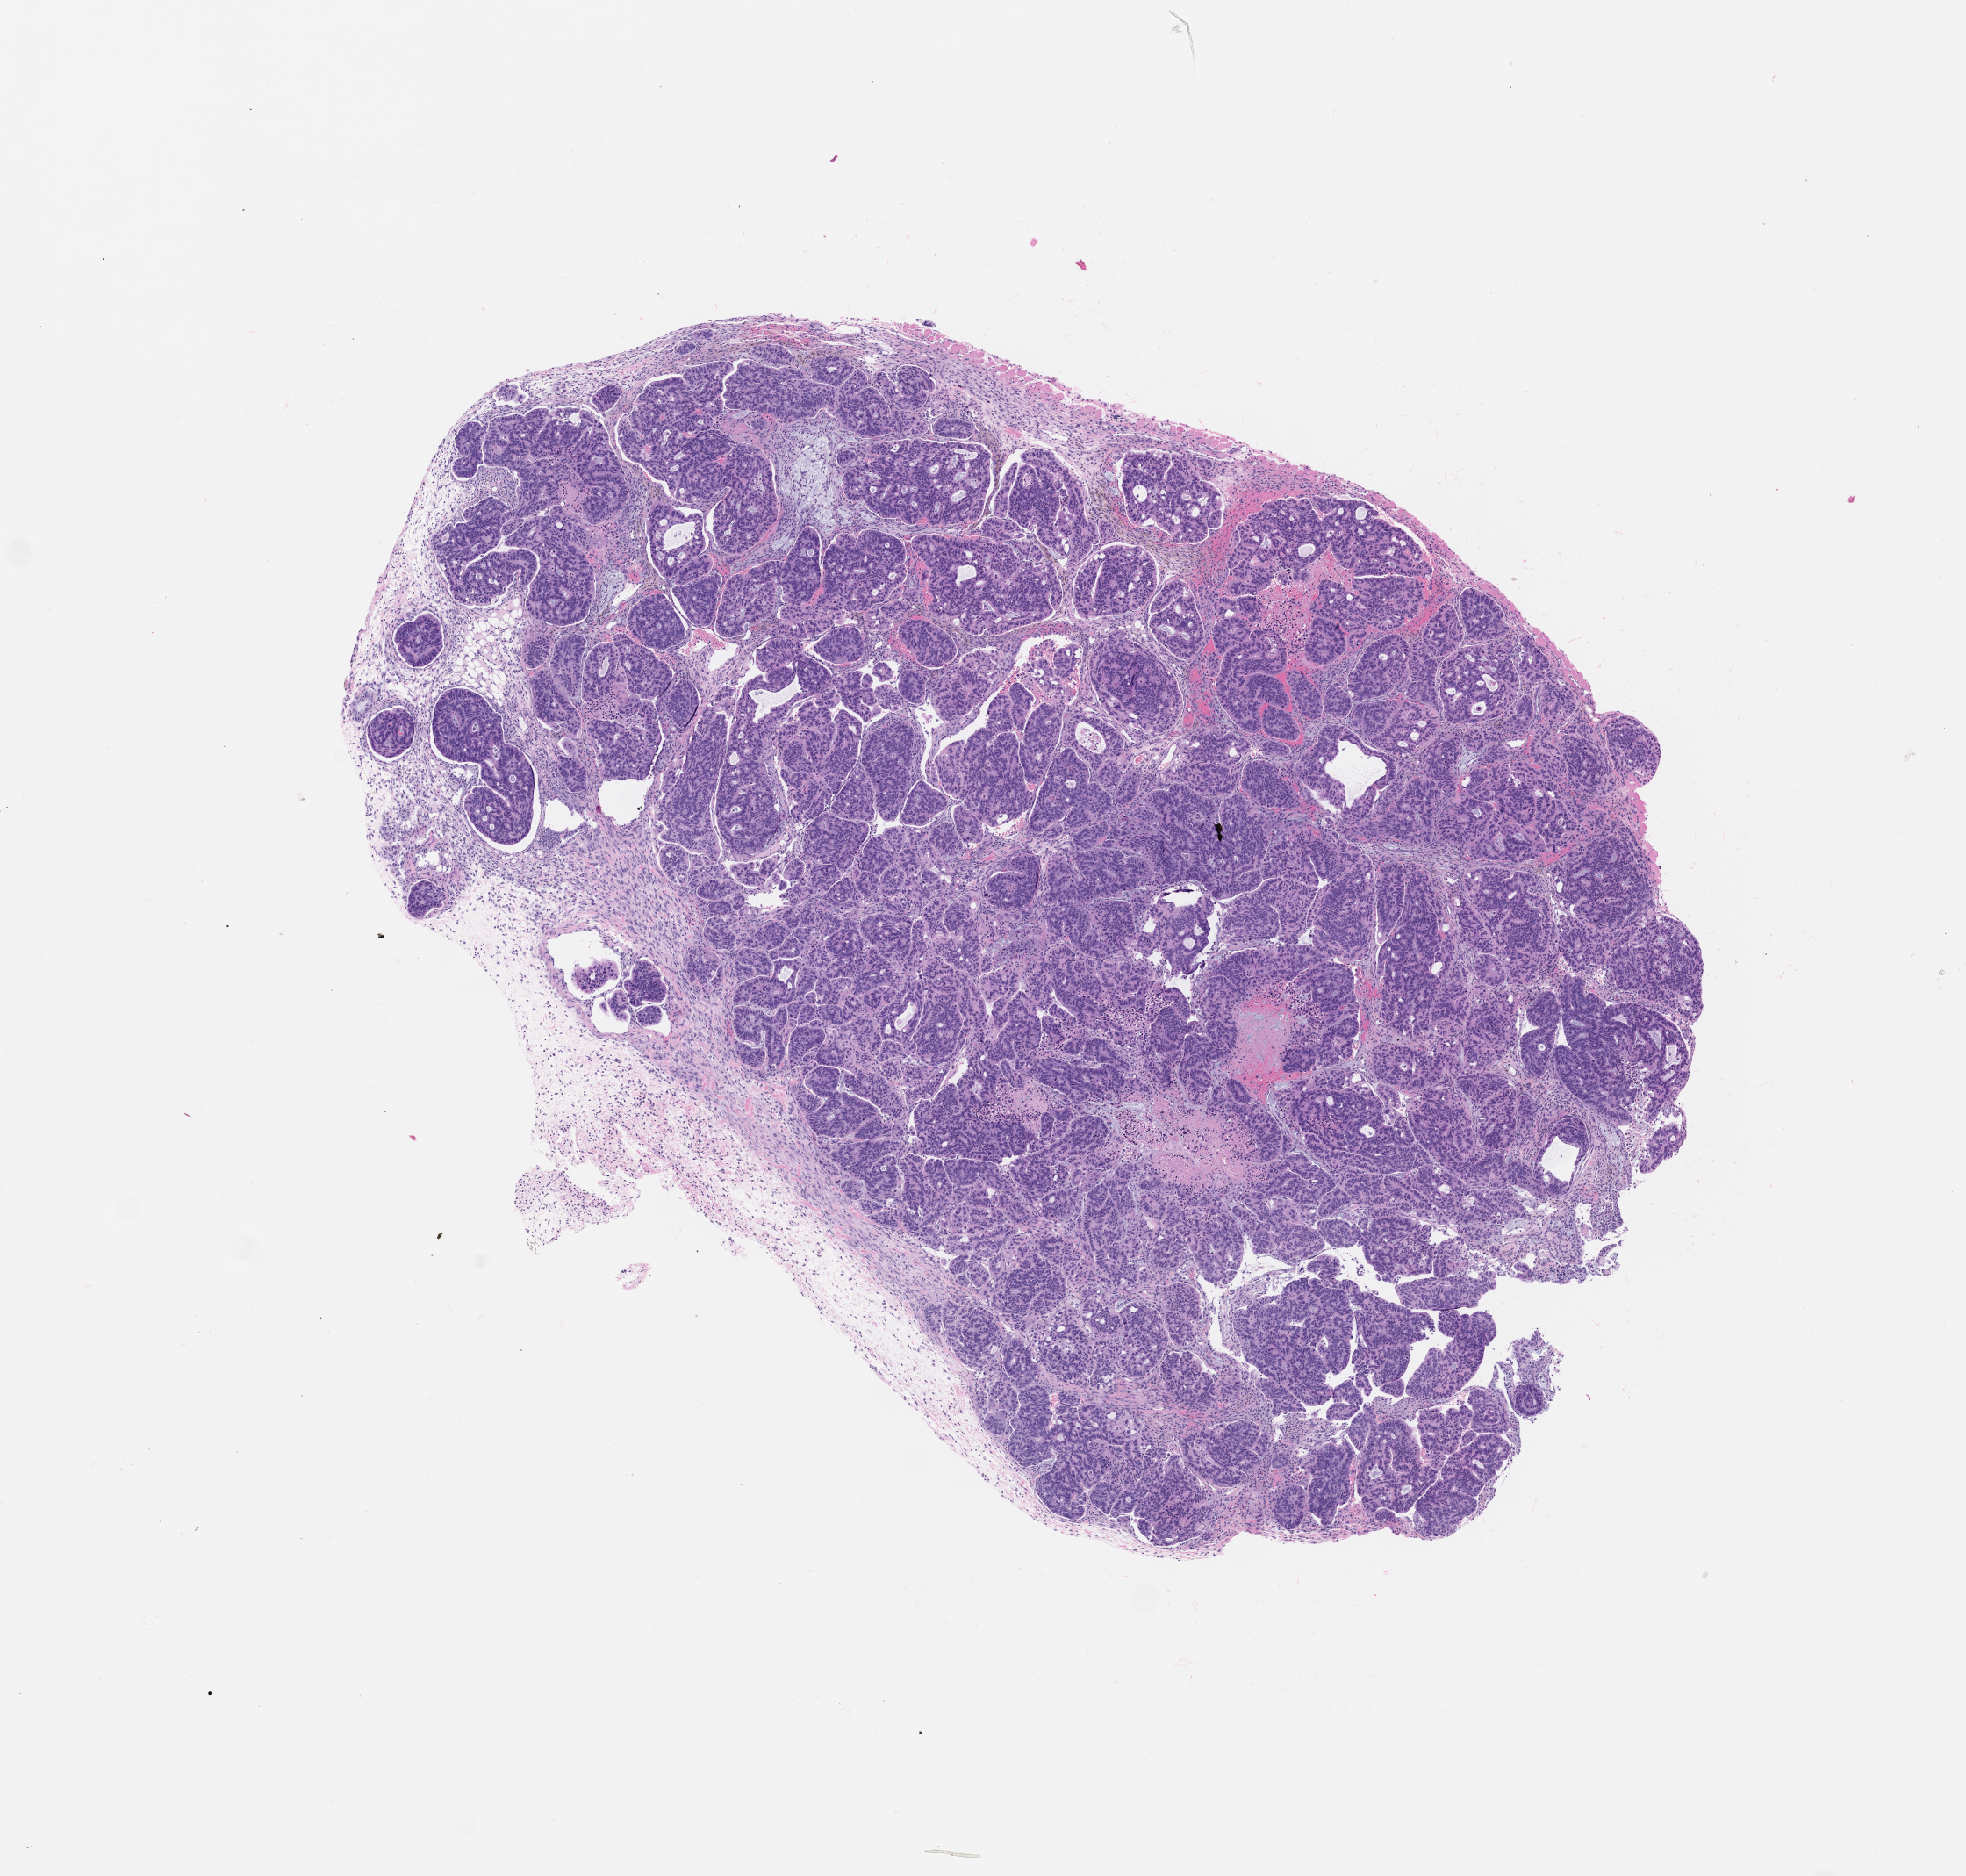
Whole-slide image, hematoxylin and eosin (H&E): patient-derived xenograft (human tumor grown in a mouse), passage 0 — whole scanned area (about 9.0 x 8.6 mm) shown as a low-resolution overview, formalin-fixed, paraffin-embedded (FFPE) tissue, originating tumor site category: colon.
• originating patient diagnosis: Colon Adenocarcinoma